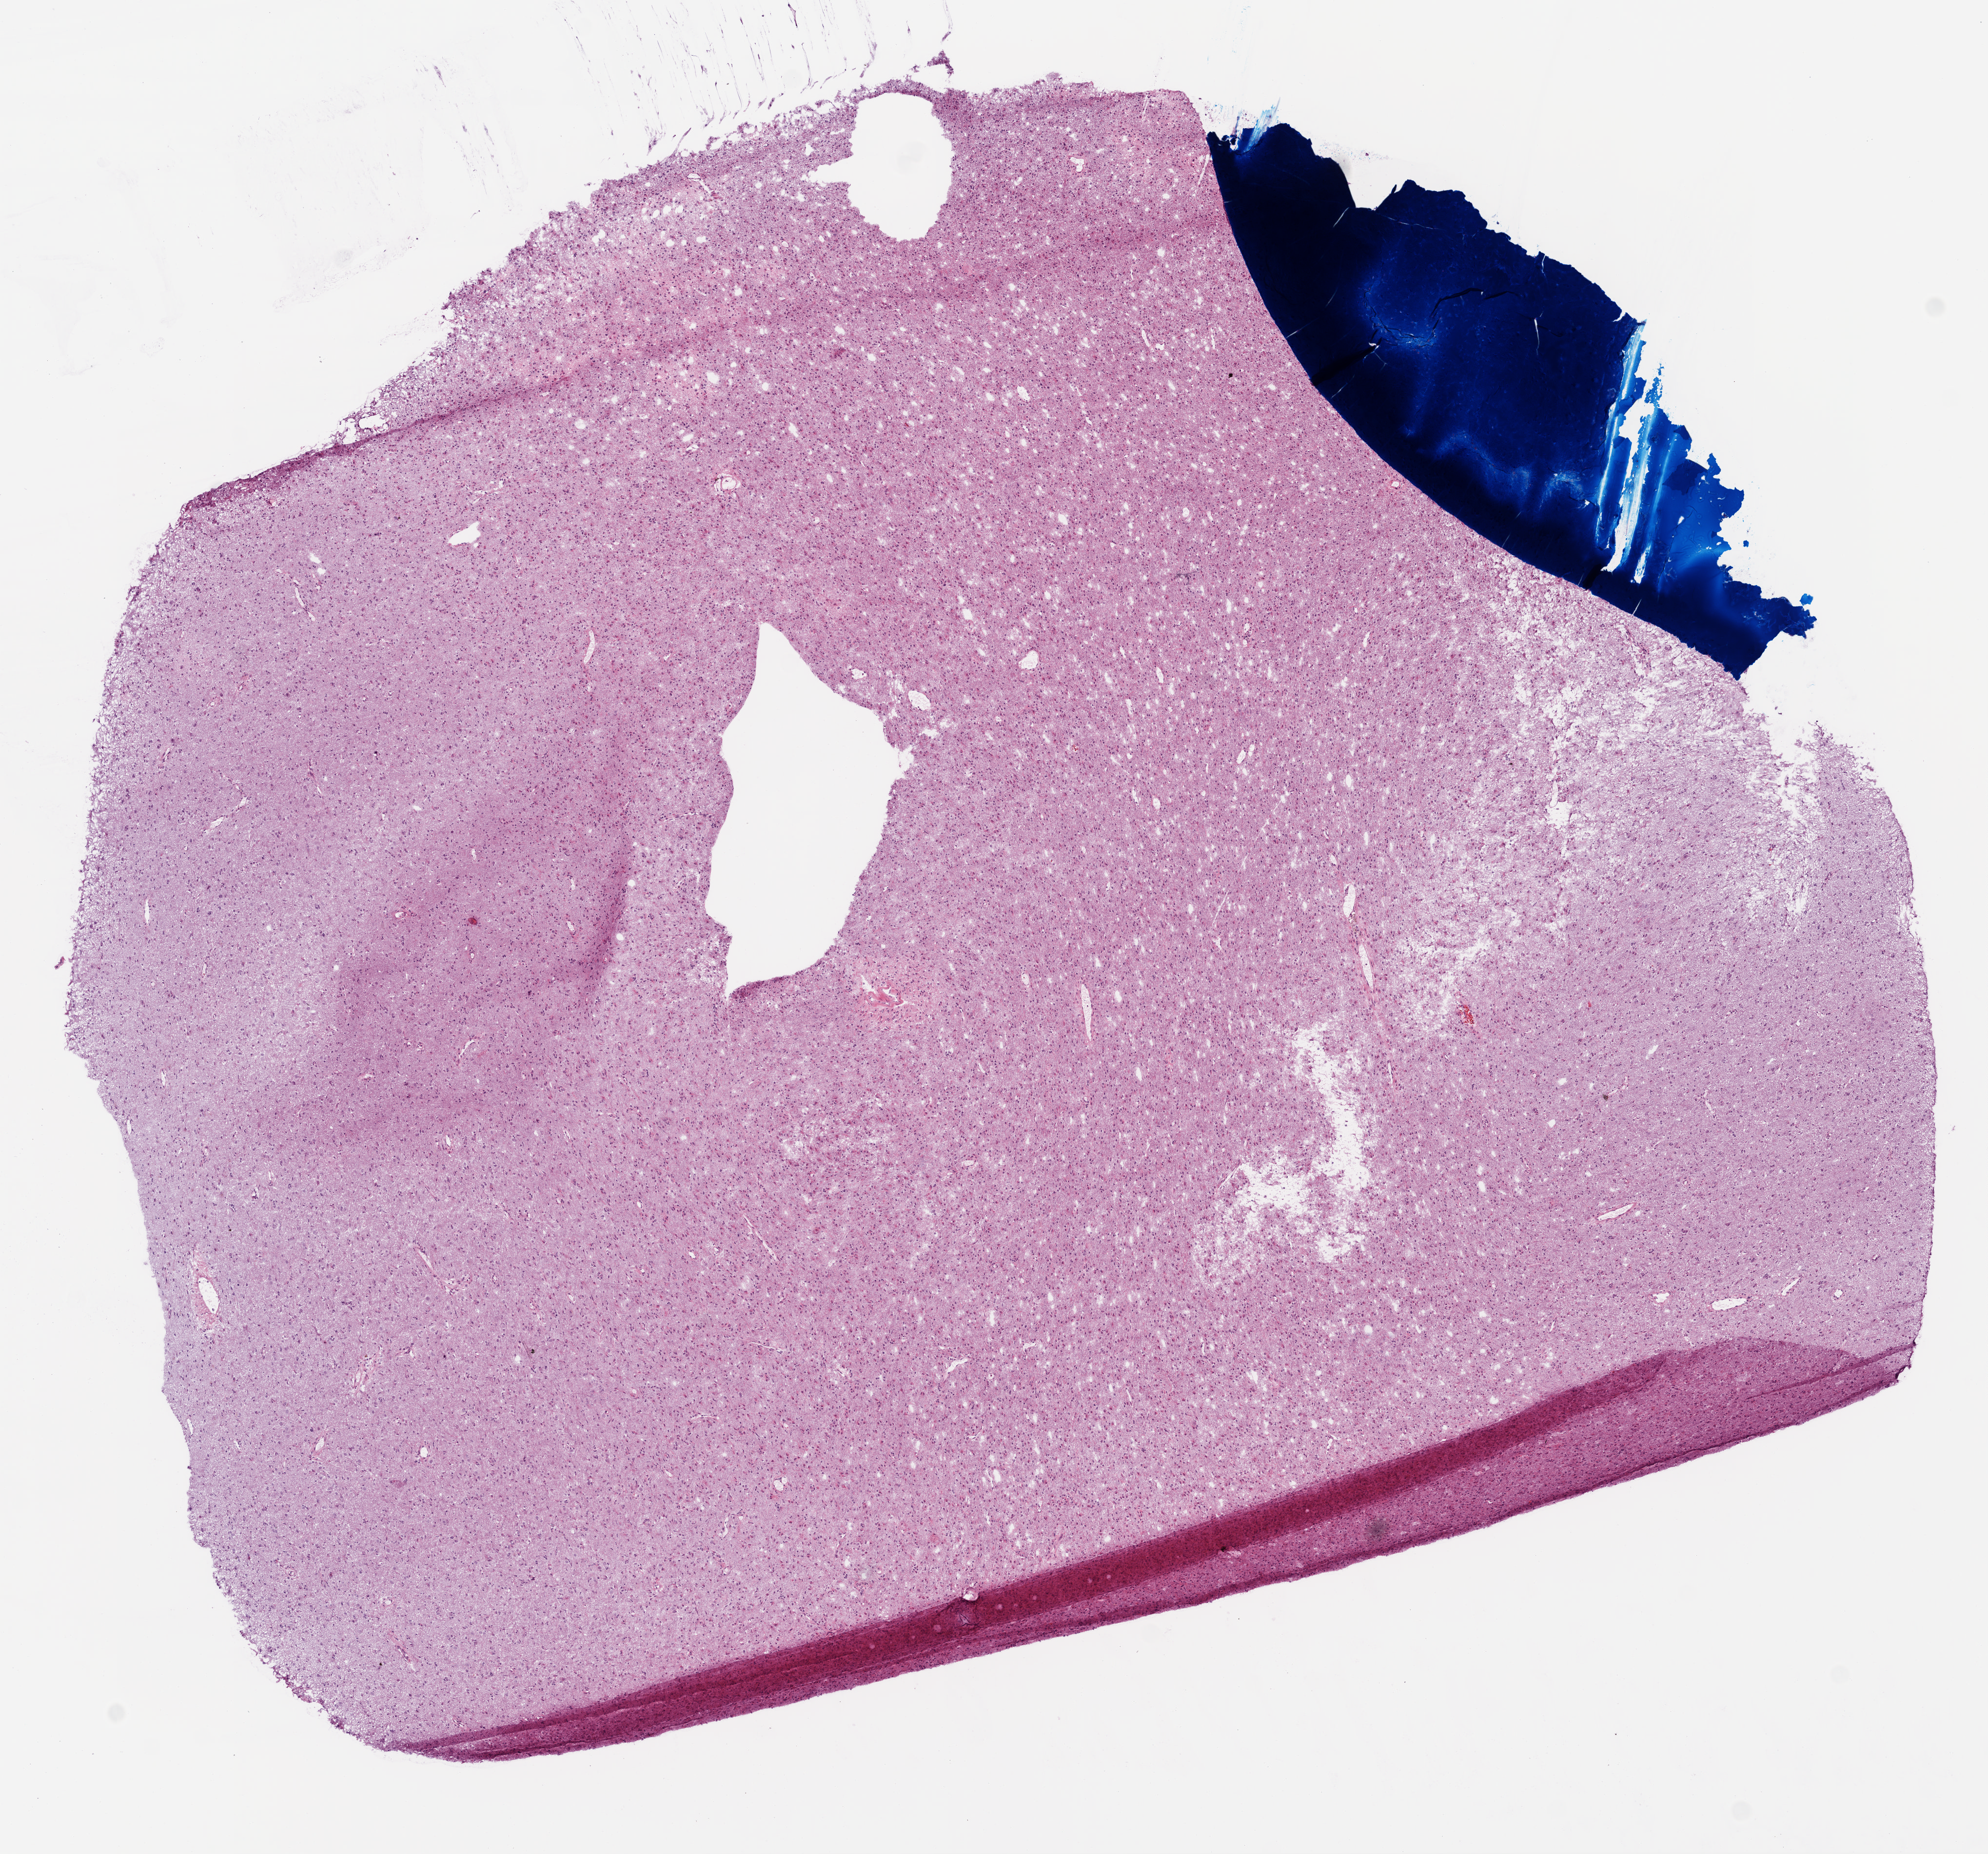
Whole-slide histology image, H&E — shown as a low-resolution overview of the whole scanned area (about 8.2 x 7.7 mm, slide scanned at 20x), frozen section, primary tumour sample from the brain. Patient: male, age at initial diagnosis 50 years. Pathologist review of this section (percent, as recorded): tumour cells 60%, tumour nuclei 80%, normal cells 0%, stromal cells 40%, necrosis 0%.
Histologic diagnosis: Glioblastoma.